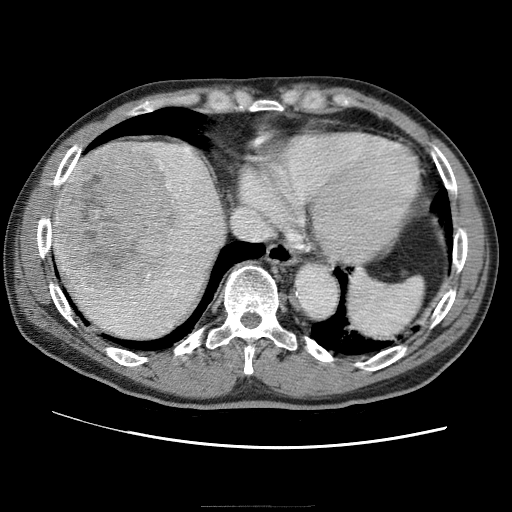
Contrast-enhanced abdominal CT (liver protocol), one axial slice; position 58 of 75 along the scan axis; 120 kVp; one of 2 acquisitions stored at this slice position; soft-tissue window (W 400 / L 40 HU); 2.5 mm slice thickness; 512 × 512 image matrix, field of view 360 × 360 mm. From the clinical record (not read from this slice): diagnosis: hepatocellular carcinoma (patient treated with transarterial chemoembolisation; whether this scan precedes or follows treatment is not stated here); TNM stage (as recorded): Stage-II; Child-Pugh class: A; tumour differentiation: well differentiated; tumour nodularity: multinodular.
Outlined on this slice (semi-automatically segmented with operator editing):
- liver parenchyma outside the tumour (the mass and vessels are separate outlines, so this box may not span the whole liver): bounding box (x1, y1, x2, y2) in pixels: (54, 140, 230, 342)
- mass: (55, 142, 182, 301)
- liver vessels: (60, 173, 183, 301)